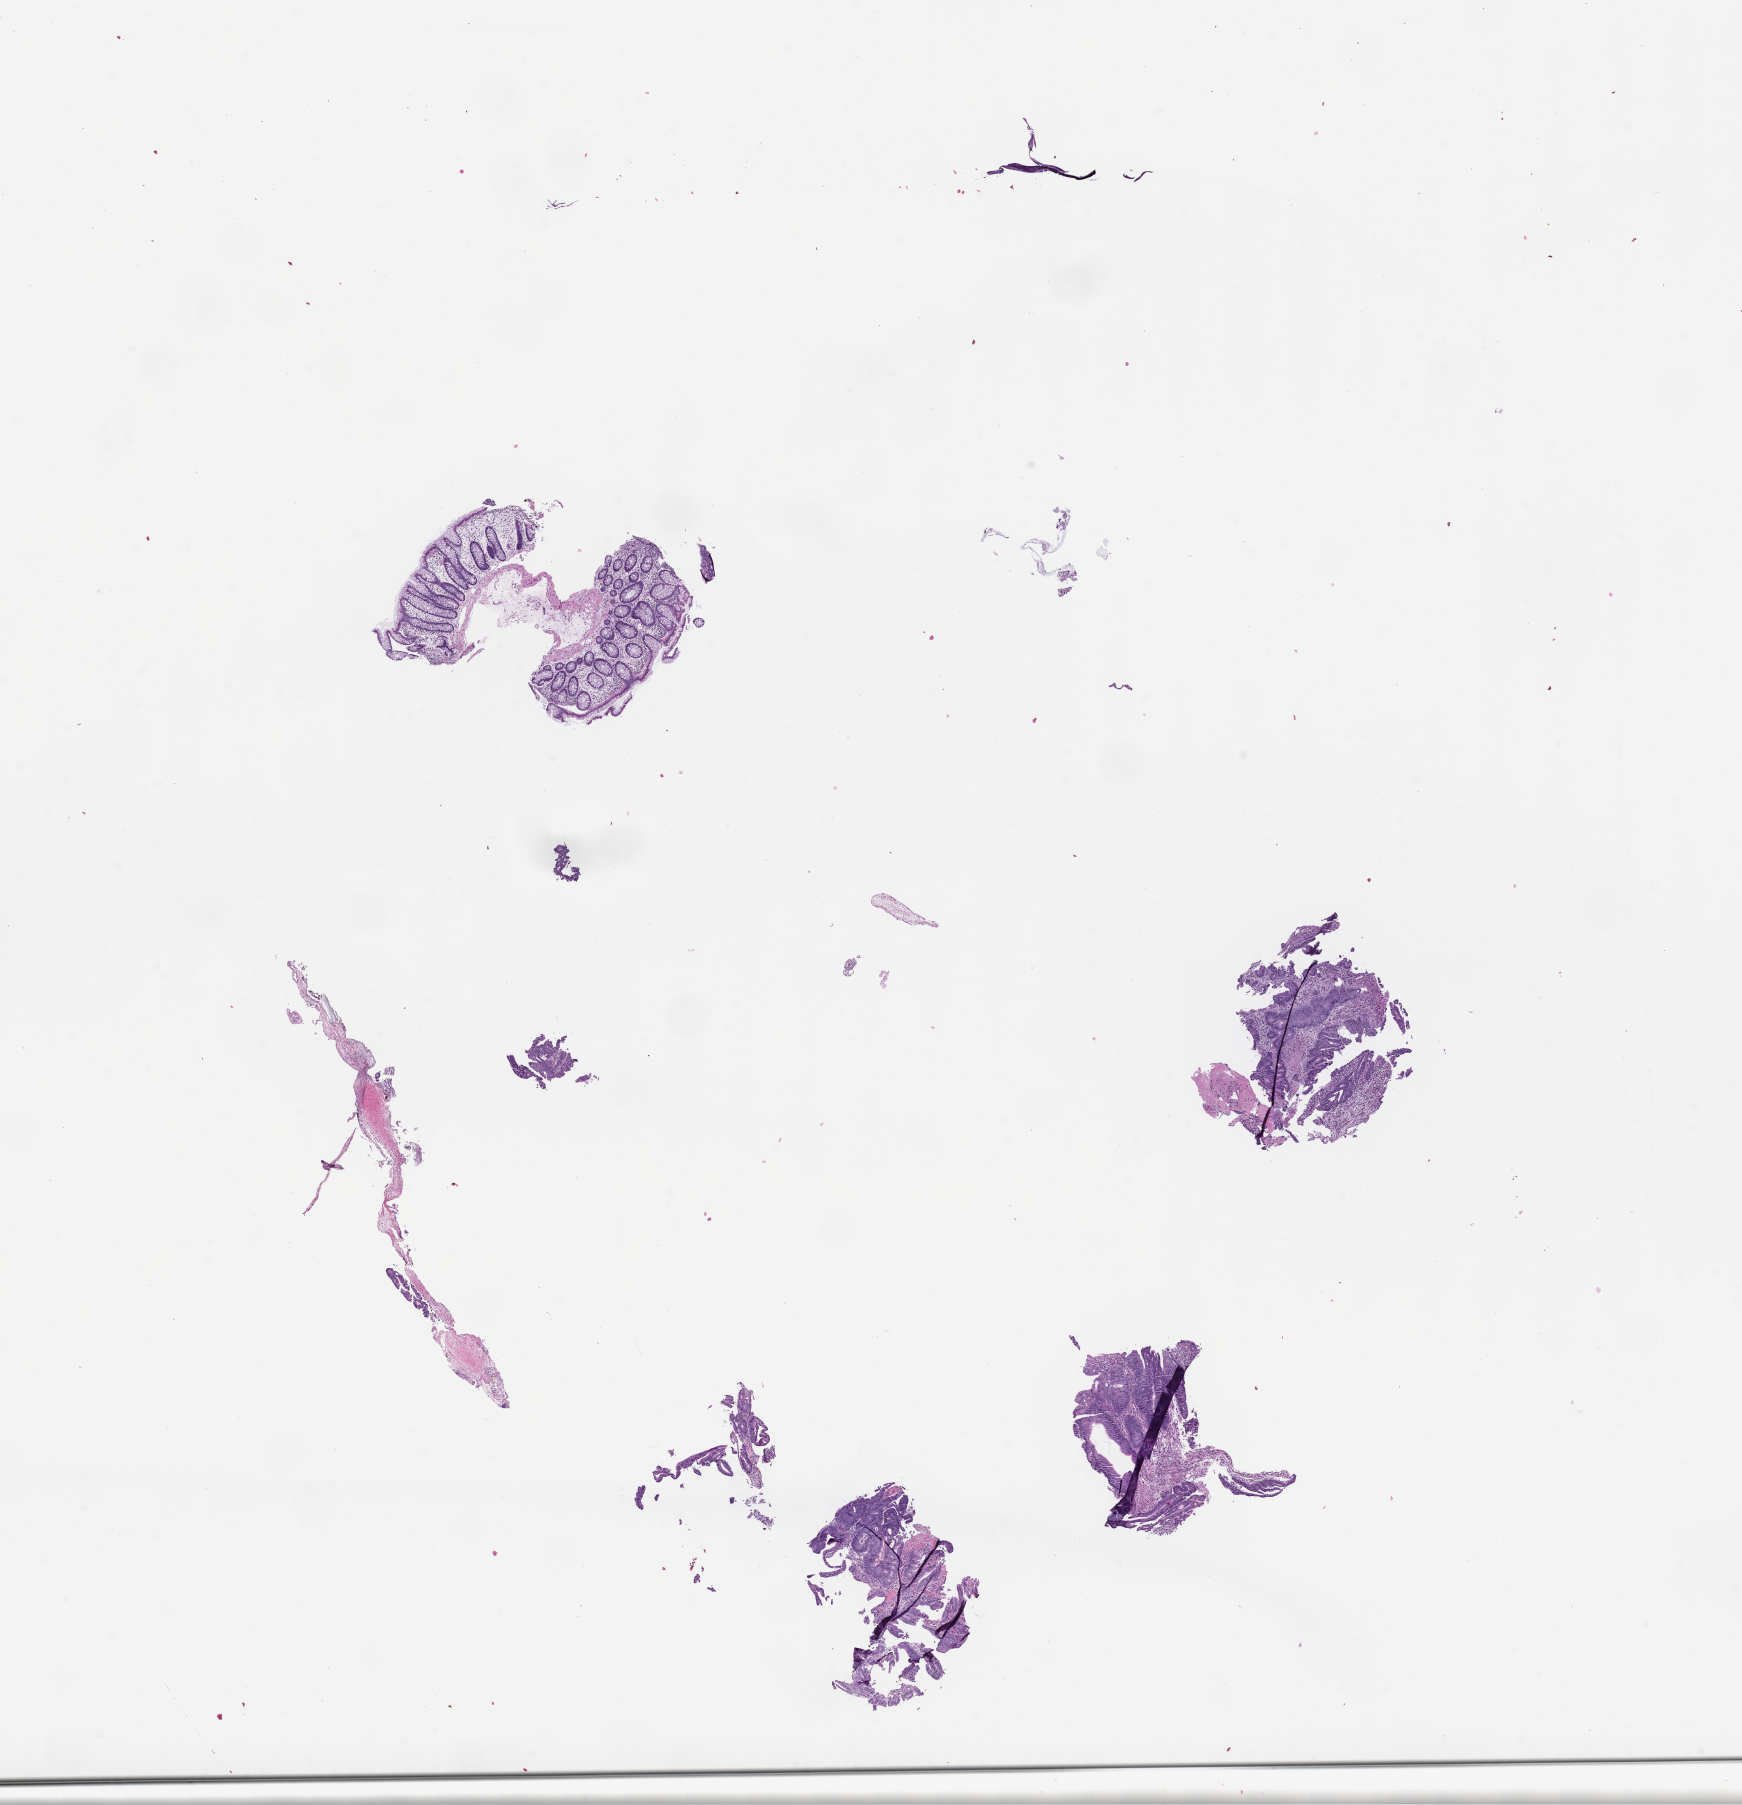
Whole-slide image, haematoxylin and eosin stain, shown as a low-resolution overview of the whole scanned area (about 14.1 x 14.6 mm). Formalin-fixed paraffin-embedded section. Tissue site: colon. Female patient.
- this section: primary tumor
- diagnosis: Colorectal Carcinoma